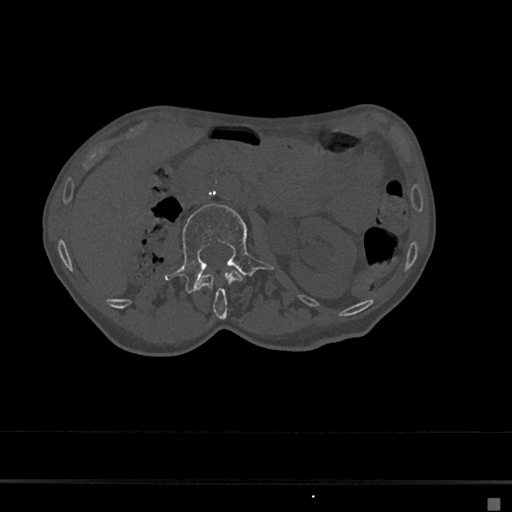
CT including the spine, one axial slice. Position 28 of 797 along the scan axis. 120 kVp. Bone window (W 1800 / L 400 HU). 0.5 mm slice thickness. 512 × 512 image matrix. Female patient, age 68 years. Case-level facts recorded for this patient, not image findings: primary cancer: renal.
Structures marked on this image (semi-automatic segmentation, software-assisted and operator-edited):
- L1 vertebra: bounding box [x1, y1, x2, y2] px = [196, 270, 243, 319]
- L2 vertebra: [164, 203, 274, 293]